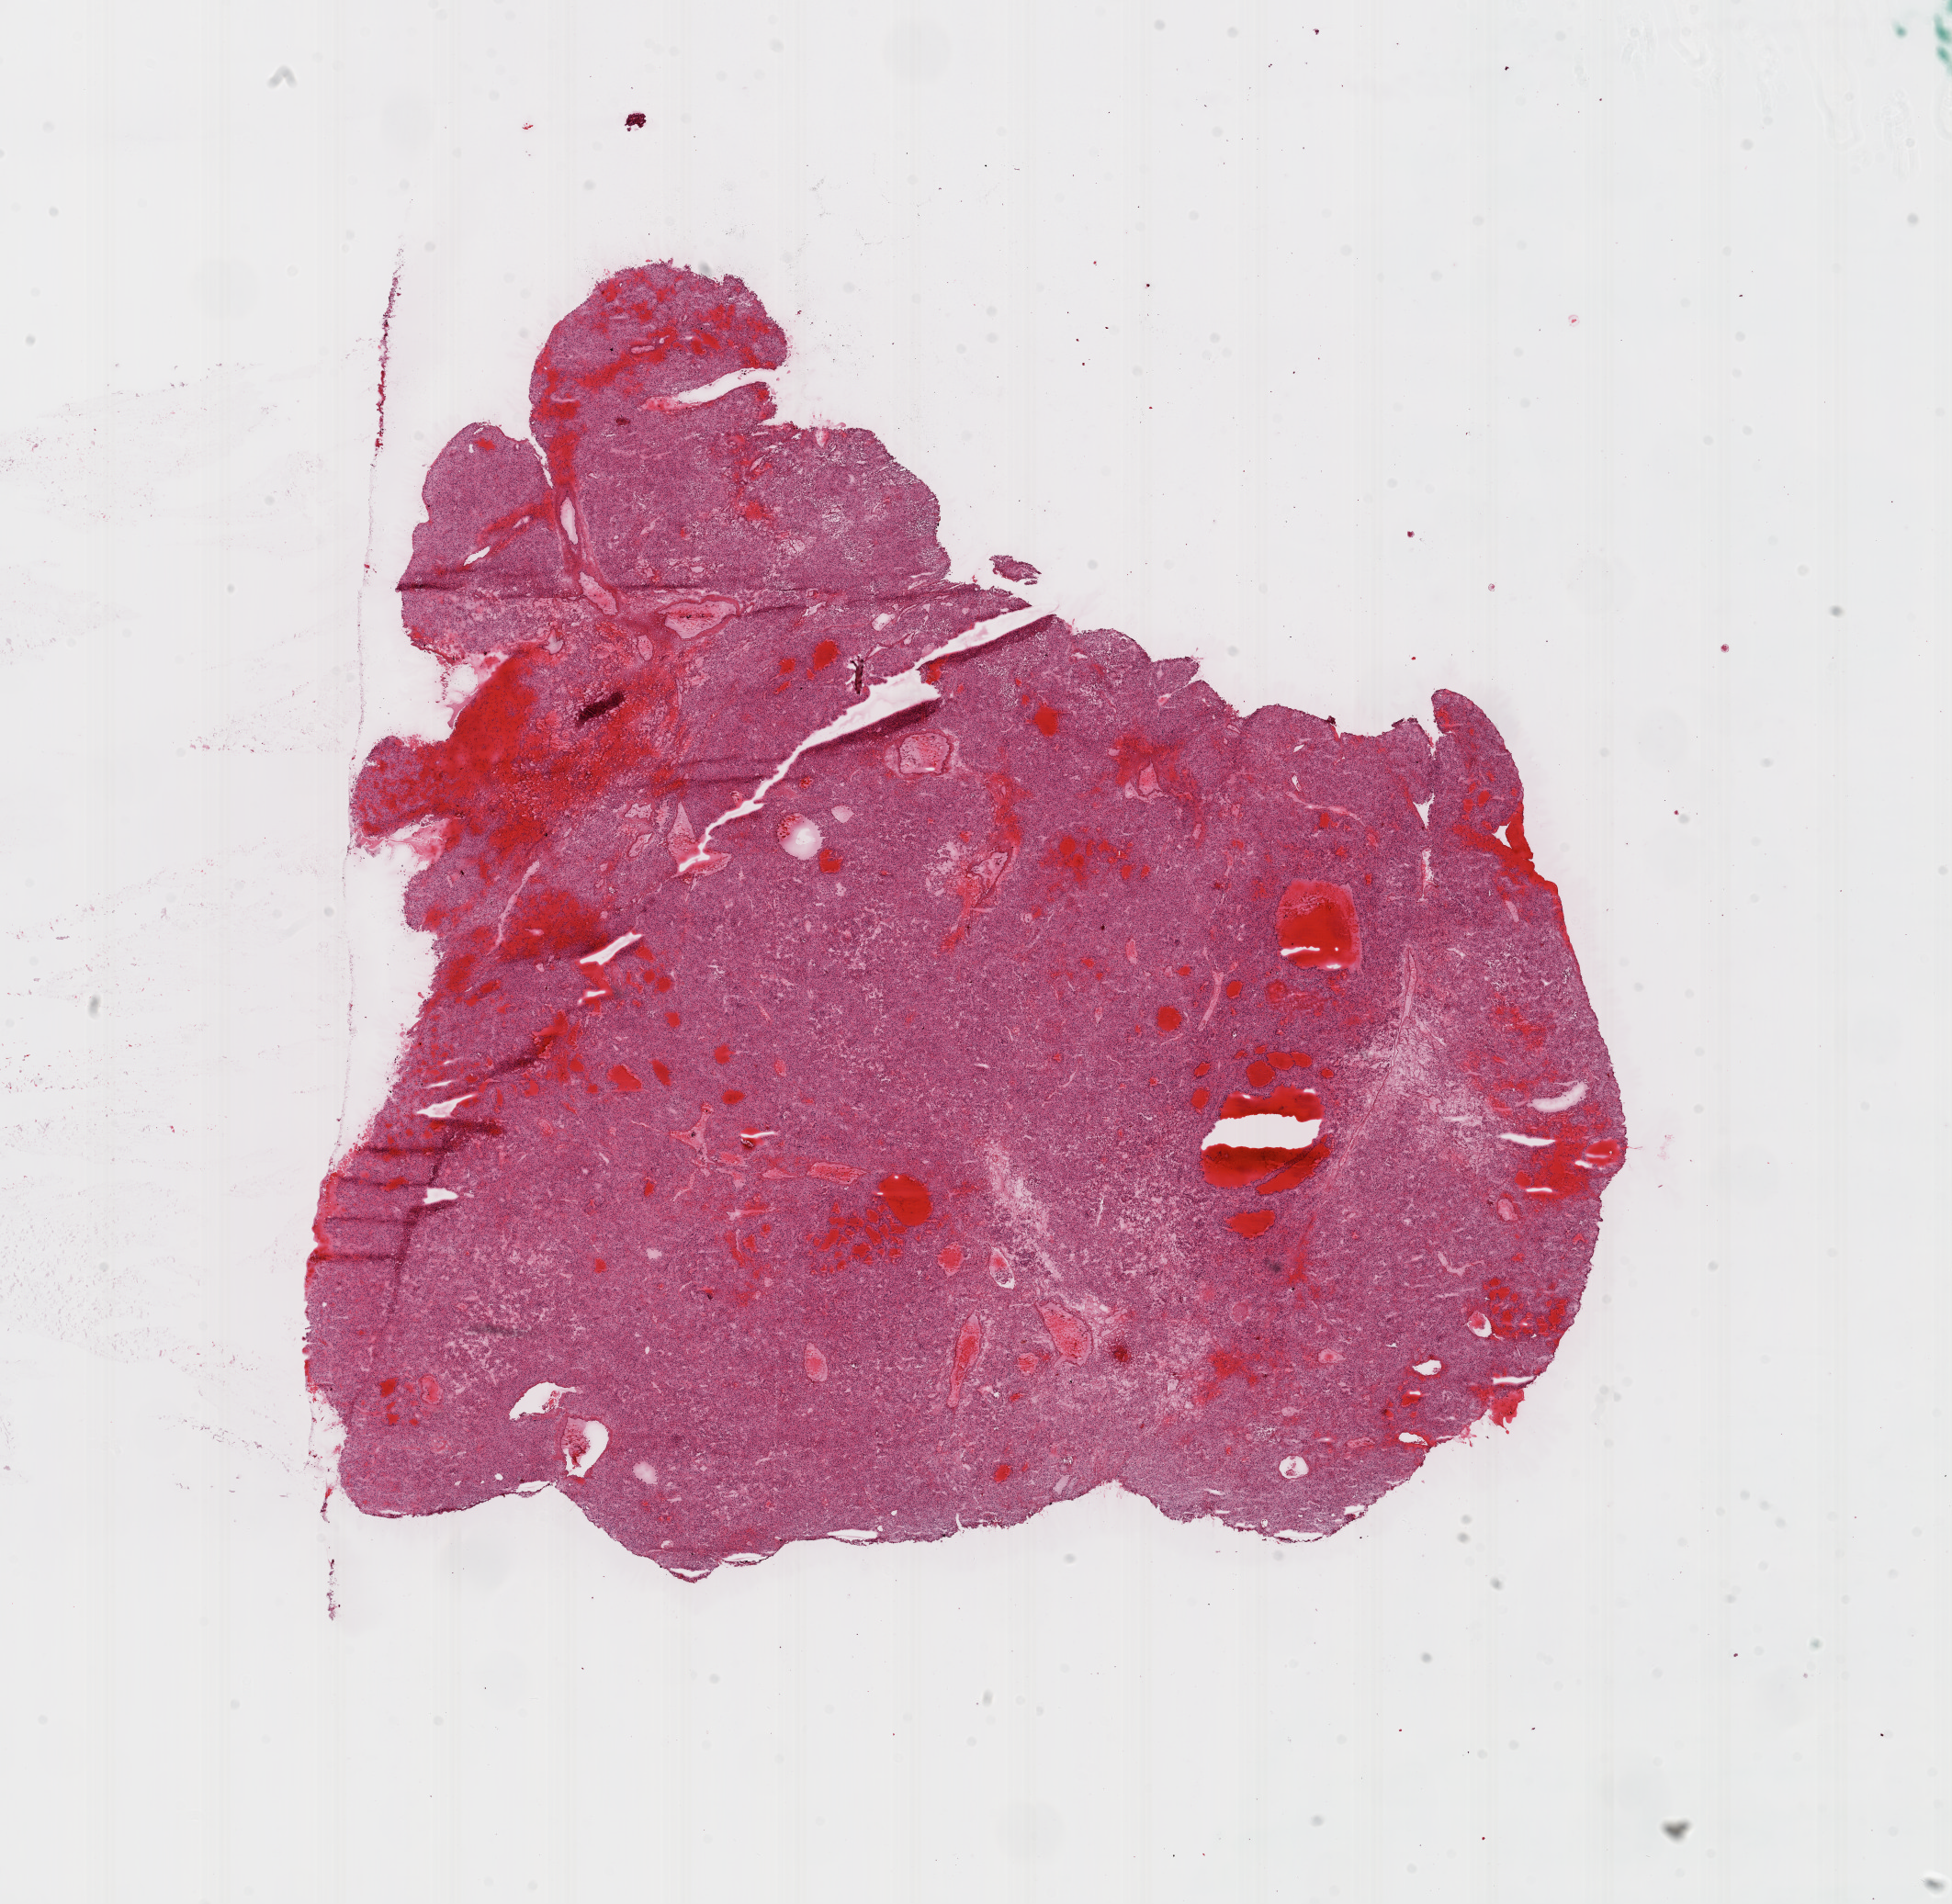
H&E whole-slide image, a low-resolution overview of the entire scanned area, about 17.1 x 16.6 mm; frozen section from the top of the tissue portion; primary tumour sample from the kidney. Male patient; age at initial diagnosis 77 years. Histologic grade: G3 (poorly differentiated). Composition of this section per pathologist review: tumour cells 90%, tumour nuclei 85%, normal cells 0%, stromal cells 10%, necrosis 0%.
• diagnosis: Clear cell adenocarcinoma, NOS
• AJCC pathologic stage: I